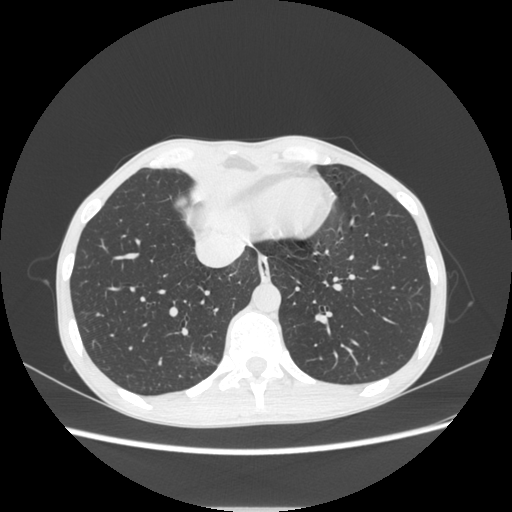
Chest CT, one axial slice; position 81 of 272 along the scan axis; 120 kVp; lung window (W 1500 / L -600 HU); 1.25 mm slice thickness; 512 × 512 image matrix, field of view 350 × 350 mm. Patient: female, 51 years. From the clinical record (not read from this slice): clinical TNM (as recorded): T1c N0 M0.
Structures marked on this image (rectangle marked by the reading radiologist):
- lung tumour (recorded histology: adenocarcinoma): bounding box [x1, y1, x2, y2] px = [185, 347, 218, 375]